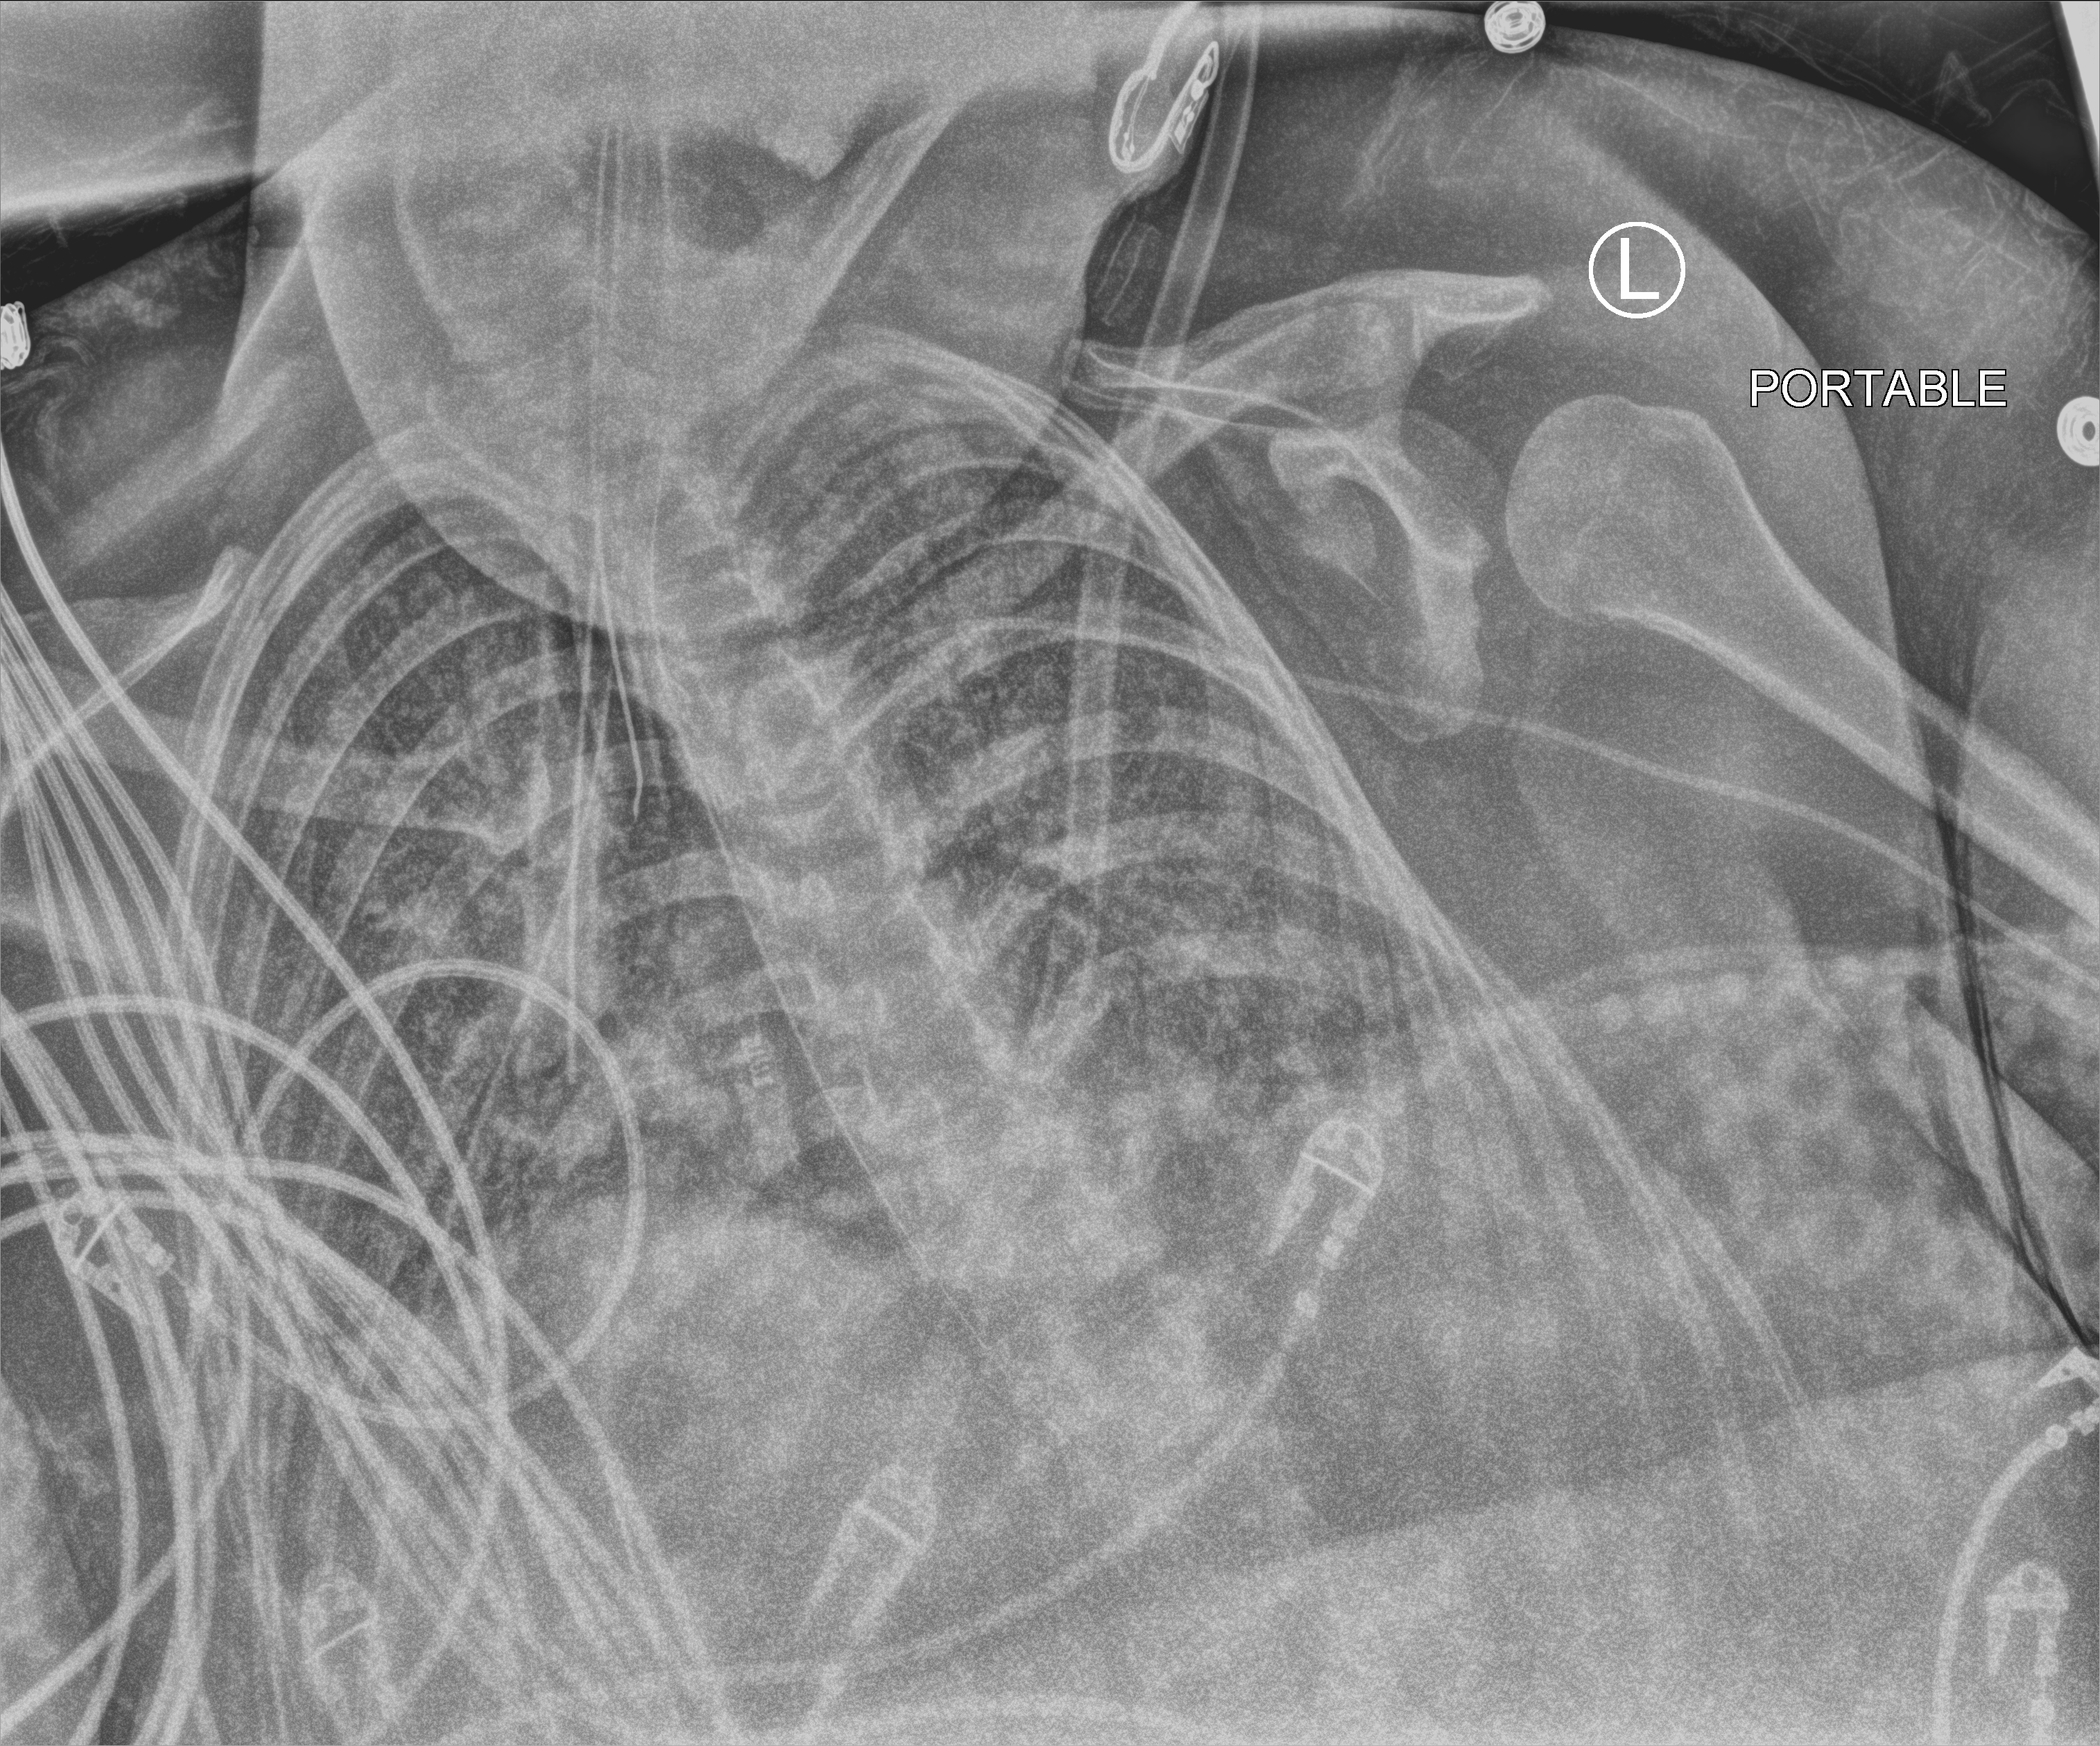
Portable chest radiograph, anteroposterior (AP) projection. Female patient hospitalised with COVID-19, age 18–59 years.
Admission-level facts for this patient (not findings on this image; timing relative to this image not recorded): hypertension (admission record): yes; admitted to intensive care during this hospital stay: yes; mechanically ventilated during this hospital stay: yes.